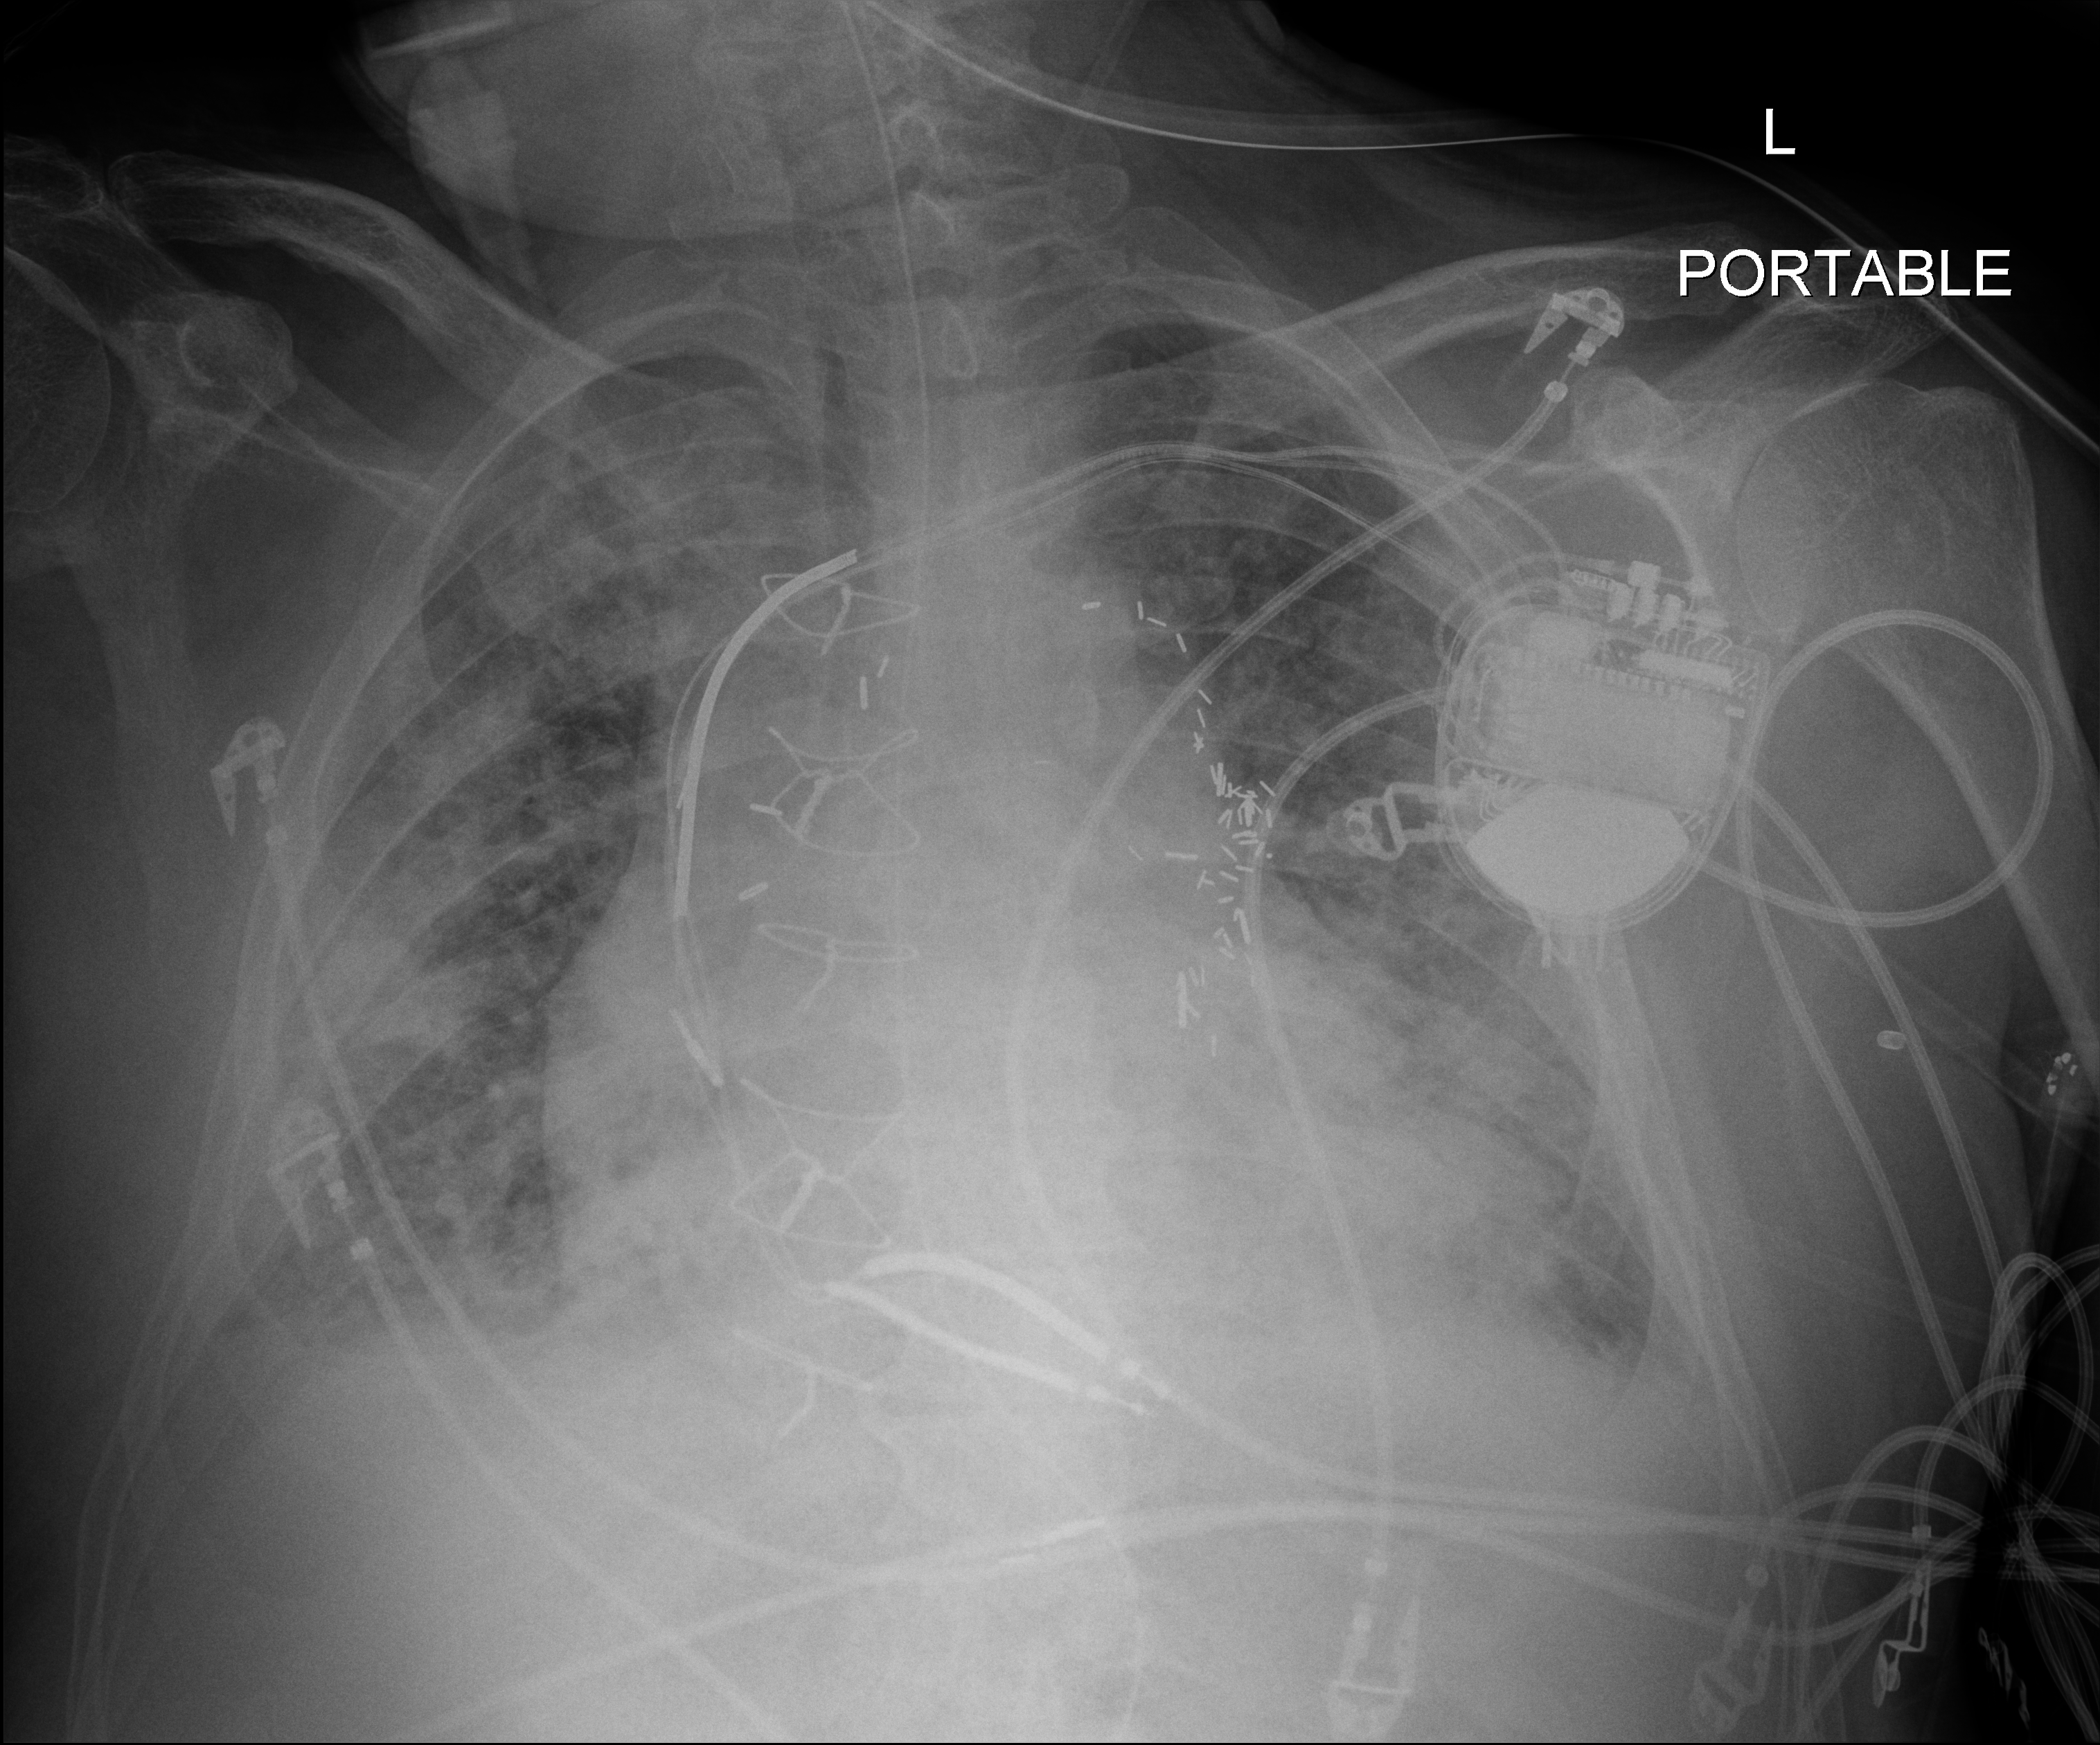
Portable chest radiograph. Patient hospitalised with COVID-19; male, aged 60–74 years.
From the hospital-stay record, not from the radiograph (when in the stay this image was taken is not recorded):
- hypertension (admission record): yes
- COPD (admission record): no
- mechanically ventilated during this hospital stay: yes